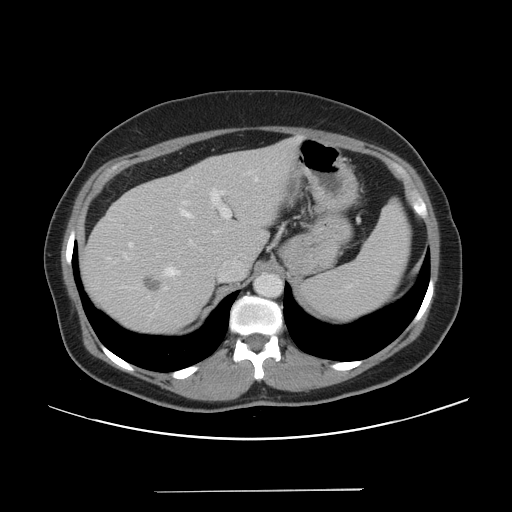
Contrast-enhanced abdominal CT, one axial slice; slice 33 of 56 in the series (ordered by position); 120 kVp; soft-tissue window (W 400 / L 40 HU); 512 × 512 image matrix, field of view 419 × 419 mm. Female patient, age 54 years. From the clinical record (not read from this slice): diagnosis: colorectal cancer liver metastases, imaged before liver resection; multiple liver metastases: yes; largest metastasis: 3.2 cm.
Outlined on this slice (manually delineated by an expert):
- hepatic veins: bounding box [x1, y1, x2, y2] px = [166, 179, 257, 276]
- liver: [81, 137, 302, 336]
- planned liver remnant (the part of the liver to remain after resection): [181, 137, 302, 265]
- portal vein (with intrahepatic branches): [209, 187, 231, 220]
- liver metastasis: [144, 275, 163, 292]